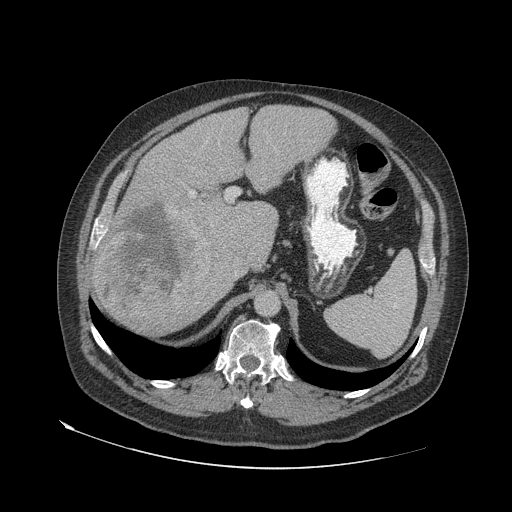
Contrast-enhanced abdominal CT (liver protocol), one axial slice. Position 43 of 79 along the scan axis. Reconstruction kernel STANDARD. 140 kVp. Soft-tissue window (W 400 / L 40 HU). 2.5 mm slice thickness. 512 × 512 image matrix, field of view 480 × 480 mm. From the clinical record (not read from this slice): diagnosis: hepatocellular carcinoma (patient treated with transarterial chemoembolisation; whether this scan precedes or follows treatment is not stated here); TNM stage (as recorded): Stage-IVA; Child-Pugh class: A; tumour differentiation: well differentiated; tumour nodularity: multinodular.
Structures marked on this image (semi-automatically segmented with operator editing):
- liver parenchyma outside the tumour (the mass and vessels are separate outlines, so this box may not span the whole liver): box from (x=92, y=104) to (x=335, y=332) px
- mass: (x=97, y=199)–(x=213, y=319)
- liver vessels: (x=95, y=191)–(x=212, y=248)